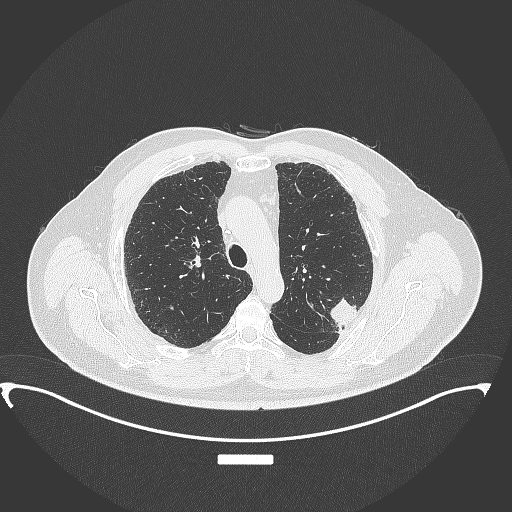
Chest CT, one axial slice; slice 262 of 350 in the series (ordered by position); reconstruction kernel B70f; 120 kVp; lung window (W 1500 / L -600 HU); 1 mm slice thickness; 512 × 512 image matrix, field of view 459 × 459 mm. Male patient, age 64 years. From the clinical record (not read from this slice): clinical TNM (as recorded): T1c N1 M1.
Annotated regions visible in this slice (bounding box drawn by a radiologist):
- lung tumour (recorded histology: adenocarcinoma): bounding box <328,297,362,327> (left, top, right, bottom; pixels)